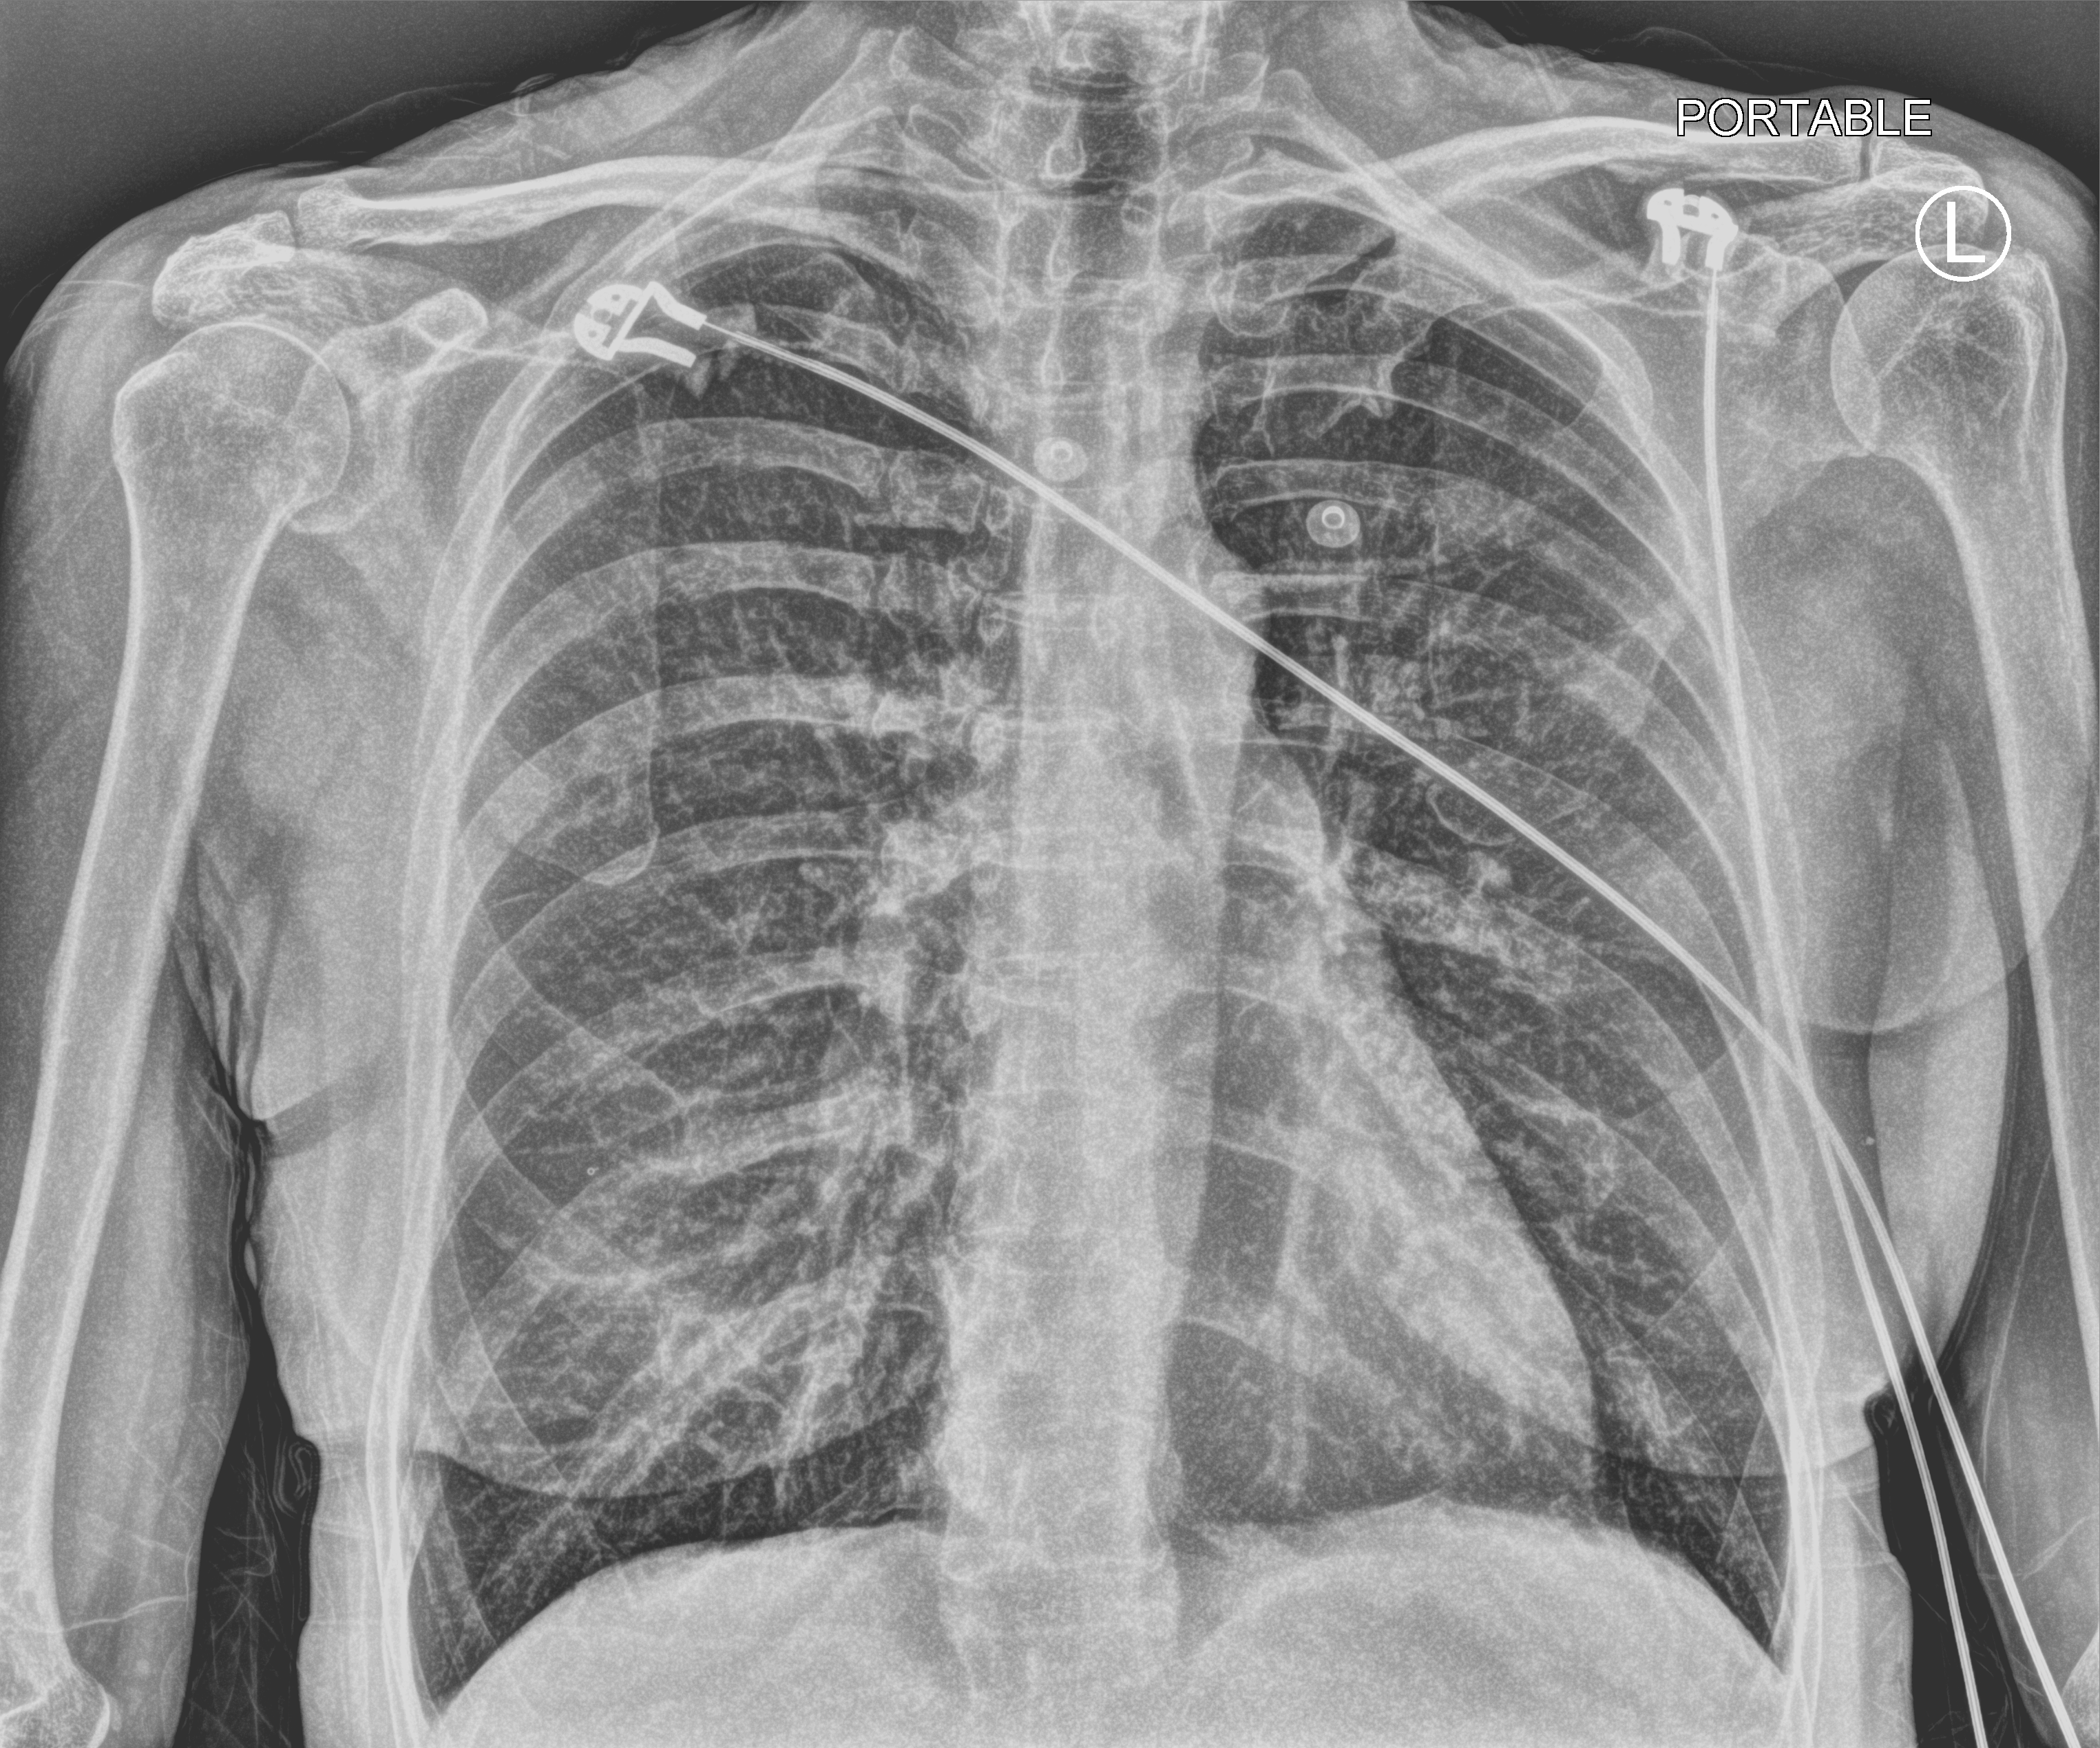
Bedside chest radiograph (computed radiography); anteroposterior (AP) projection. Patient hospitalised with COVID-19; female, aged 18–59 years.
Hospital-stay facts (about this admission, not read from this image; timing relative to this image not recorded):
- chronic kidney disease (admission record): no